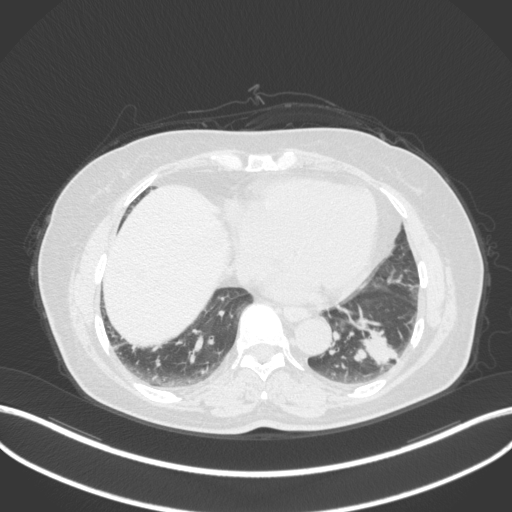
Chest CT, one axial slice; slice 125 of 307 in the series (ordered by position); reconstruction kernel B31f; 120 kVp; lung window (W 1500 / L -600 HU); 512 × 512 image matrix, field of view 400 × 400 mm. Patient: female, 59 years. From the clinical record (not read from this slice): clinical TNM (as recorded): T2a N0 M0; histopathological grade: G2-3.
Structures marked on this image (bounding box drawn by a radiologist):
- lung tumour (recorded histology: adenocarcinoma): bounding box <345,325,403,372> (left, top, right, bottom; pixels)